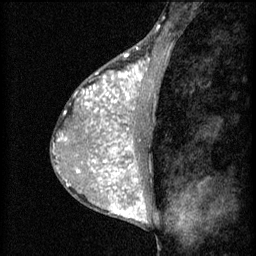
Breast MRI (dynamic contrast-enhanced), one sagittal slice. 3 images stored at this slice position (order not interpretable as contrast timing). 1.5 T. TE 4.2 ms, TR 8.2 ms. 2 mm slice thickness. 256 × 256 image matrix, field of view 180 × 180 mm. Patient: female, 38 years.
Annotated regions visible in this slice (semi-automatically segmented with operator editing):
- analysis volume of interest (the breast-tissue region the enhancement analysis was run in; not a lesion): bounding box (x1, y1, x2, y2) in pixels: (95, 106, 154, 171)
- tumour enhancement mask (voxels above the 70 % enhancement threshold inside the analysis volume of interest): (95, 106, 139, 171)